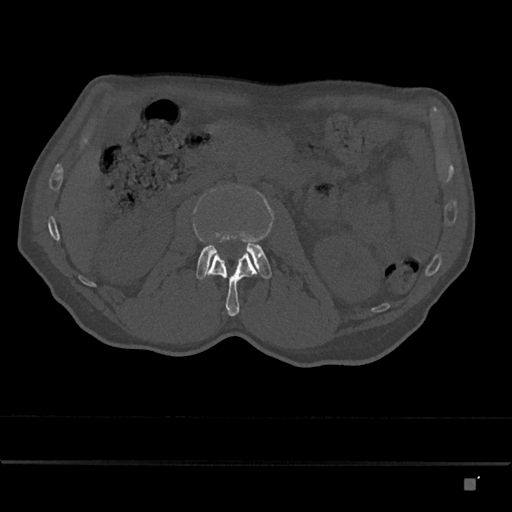
CT including the spine, one axial slice. Position 443 of 797 along the scan axis. Reconstruction kernel Br40s/3. Bone window (W 1800 / L 400 HU). 512 × 512 image matrix. Patient: male, 72 years. From the clinical record (not read from this slice): primary cancer: prostate.
Annotated regions visible in this slice (semi-automatic segmentation, software-assisted and operator-edited):
- L2 vertebra: box from (x=205, y=250) to (x=257, y=317) px
- L3 vertebra: (x=196, y=232)–(x=272, y=280)